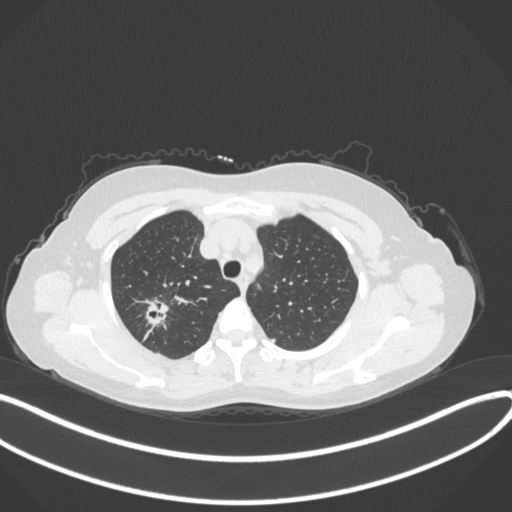
Chest CT, one axial slice; position 292 of 342 along the scan axis; reconstruction kernel B31f; 120 kVp; lung window (W 1500 / L -600 HU); 1 mm slice thickness; 512 × 512 image matrix, field of view 400 × 400 mm. Female patient, age 50 years. Case-level facts recorded for this patient, not image findings: clinical TNM (as recorded): T1c N0 M0.
Structures marked on this image (bounding box drawn by a radiologist):
- lung tumour (recorded histology: adenocarcinoma): bounding box (x1, y1, x2, y2) in pixels: (144, 293, 171, 326)